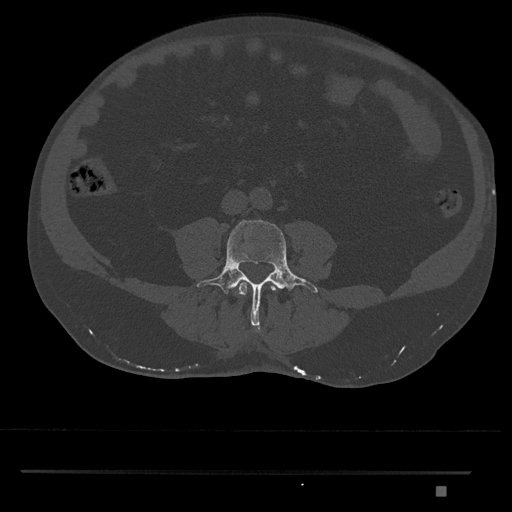
CT including the spine, one axial slice; bone window (W 1800 / L 400 HU); 0.5 mm slice thickness; 512 × 512 image matrix, field of view 429 × 429 mm. Patient: male, 65 years. From the clinical record (not read from this slice): primary cancer: prostate.
Structures marked on this image (semi-automatically segmented with operator editing):
- L3 vertebra: bounding box [x1, y1, x2, y2] px = [235, 282, 279, 296]
- L4 vertebra: [197, 219, 318, 332]